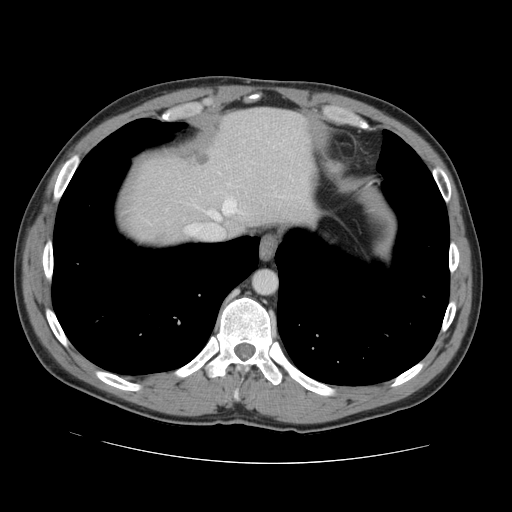
Contrast-enhanced abdominal CT, one axial slice; position 123 of 131 along the scan axis; 120 kVp; intravenous contrast given; soft-tissue window (W 400 / L 40 HU); 512 × 512 image matrix, field of view 380 × 380 mm. Male patient, age 40 years. Case-level facts recorded for this patient, not image findings: diagnosis: colorectal cancer liver metastases, imaged before liver resection; multiple liver metastases: yes; largest metastasis: 2.9 cm; disease in both lobes: yes.
Structures marked on this image (outlined manually by an expert reader):
- hepatic veins: box from (x=186, y=200) to (x=236, y=235) px
- liver: (x=131, y=109)–(x=310, y=244)
- planned liver remnant (the part of the liver to remain after resection): (x=139, y=109)–(x=311, y=233)